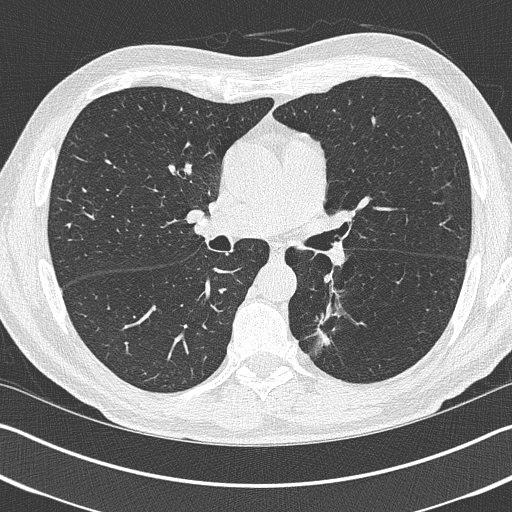
Low-dose screening chest CT, one axial slice; reconstruction kernel B50f; 120 kVp; lung window (W 1500 / L -600 HU); 1 mm slice thickness; 512 × 512 image matrix.
Outlined on this slice (expert manual segmentation):
- lesion 1 (tumor, lower lobe of left lung): bounding box [x1, y1, x2, y2] px = [313, 313, 330, 346]